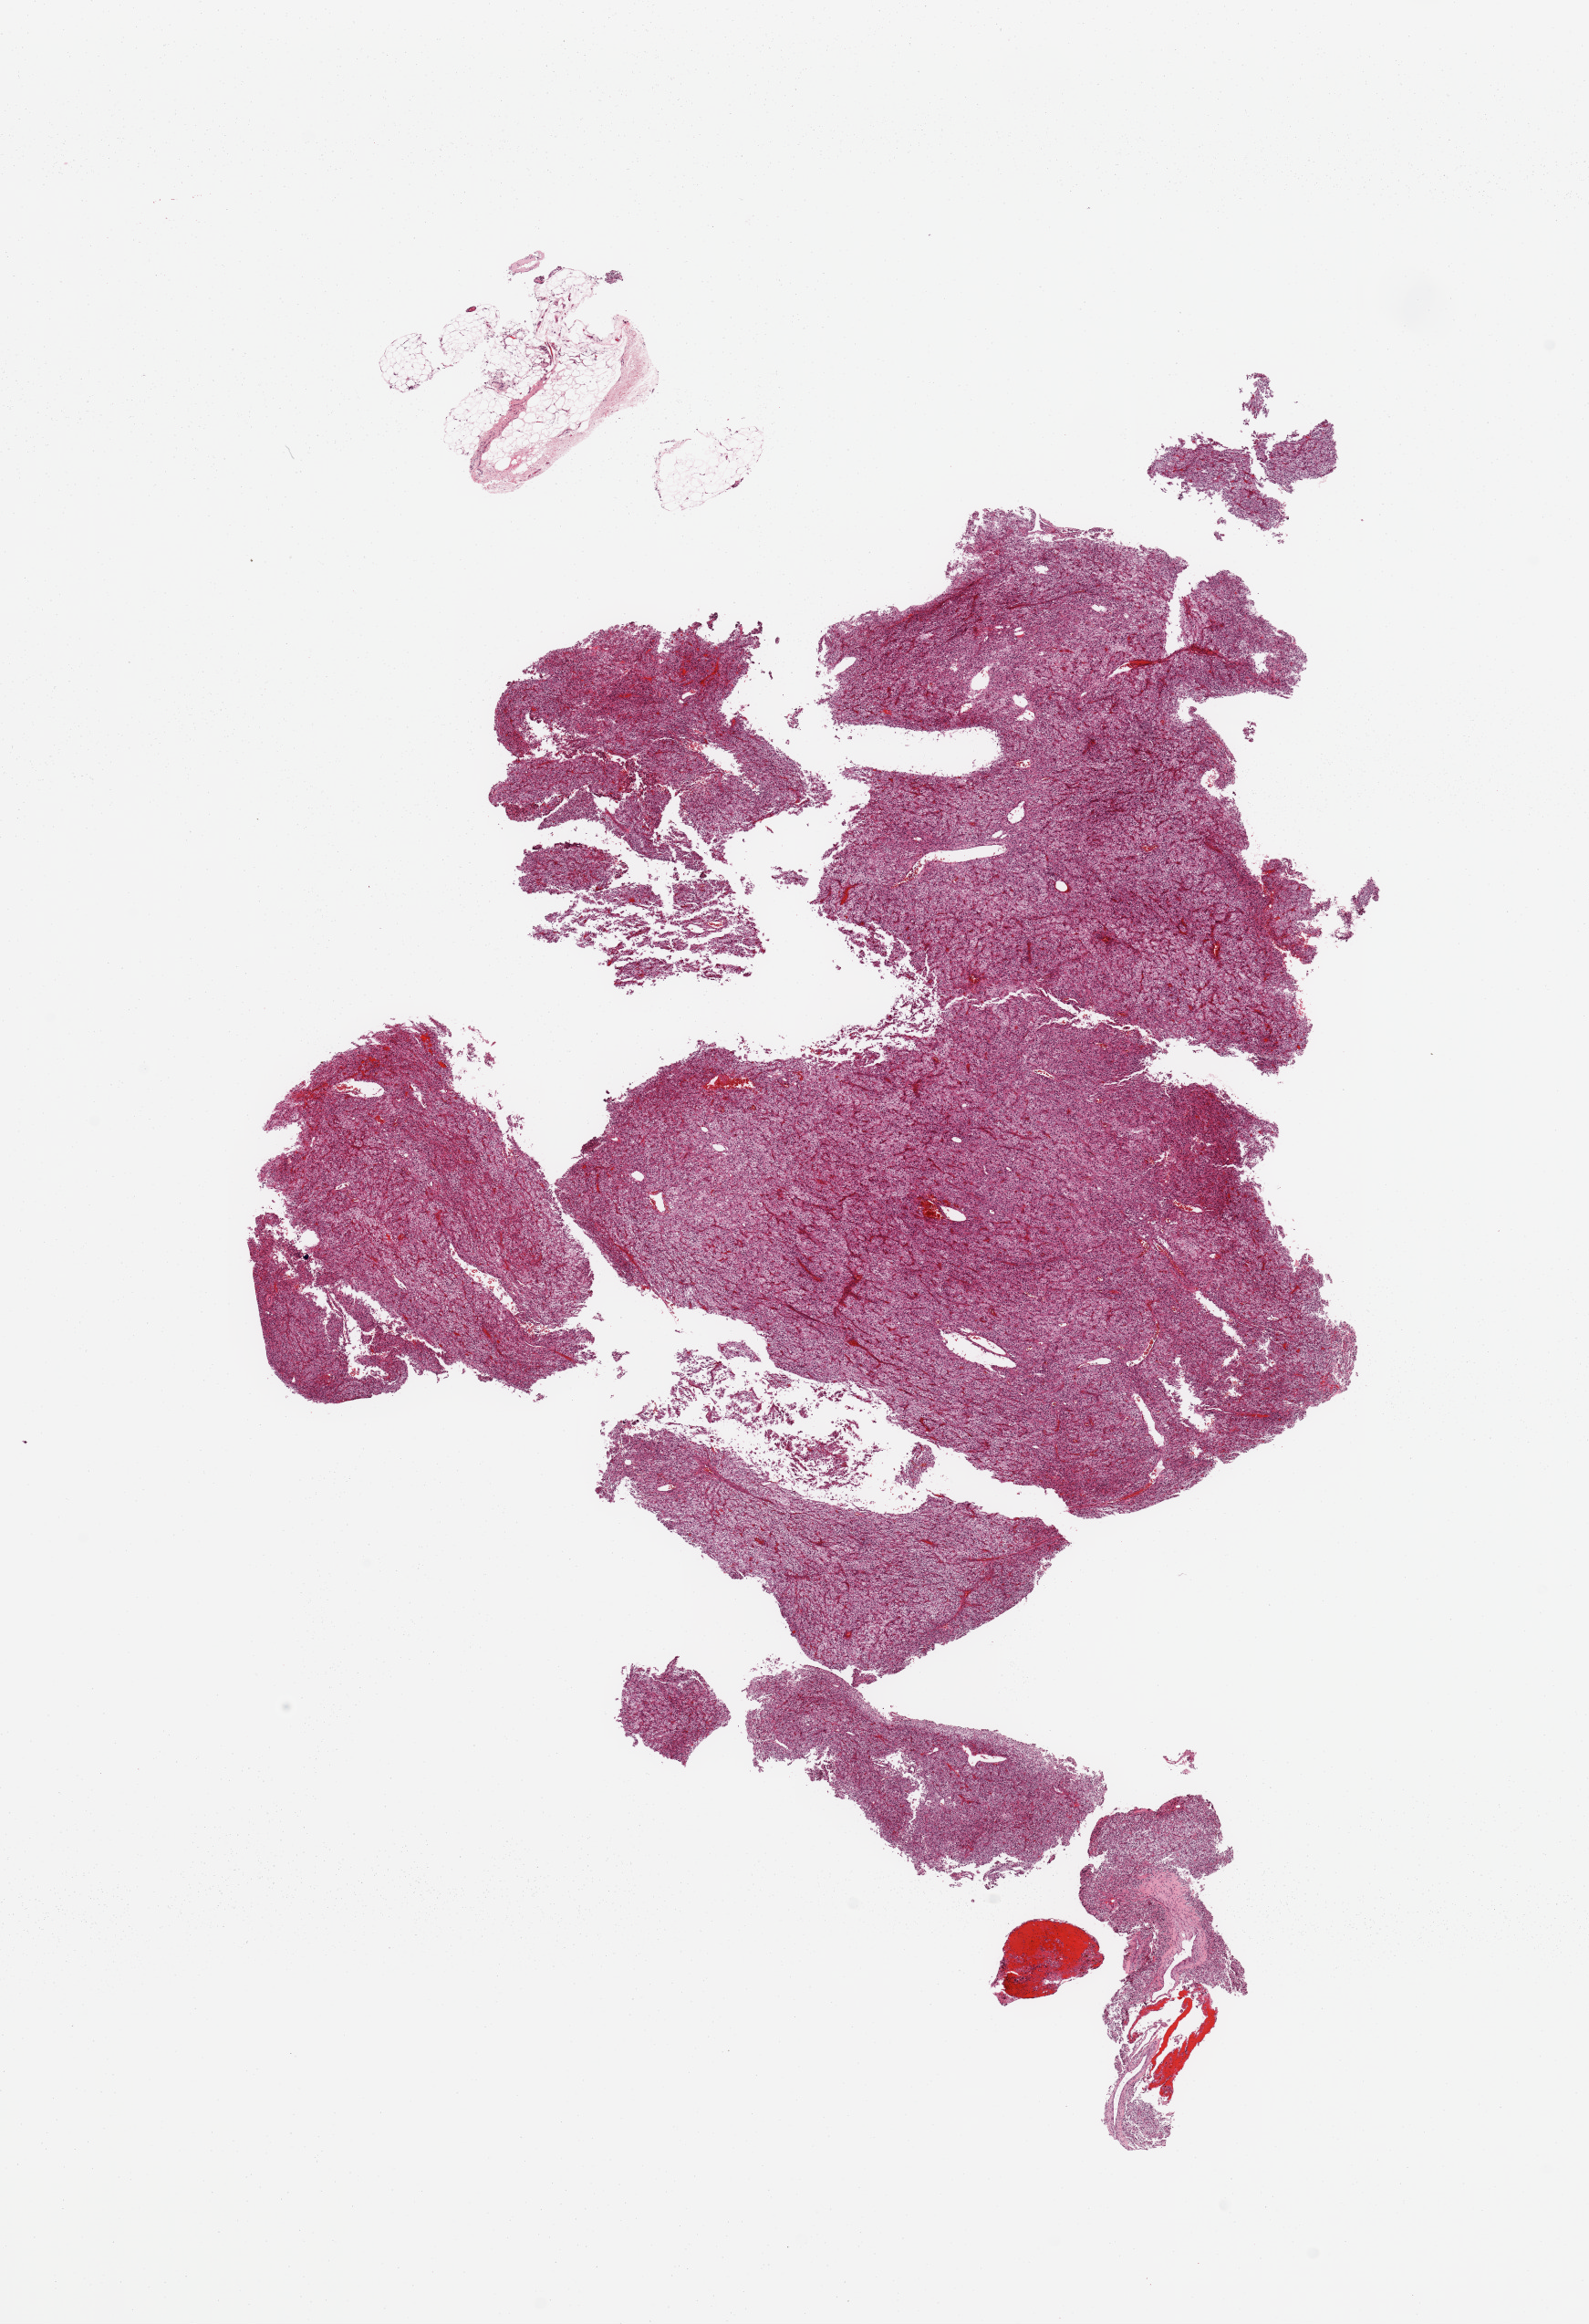
Whole-slide histology image, H&E — whole scanned area (about 13.8 x 20.2 mm, acquisition: 20x scan) shown as a low-resolution overview, tumour tissue sample, sampled site: kidney. Patient: male, age 58 years. Histologic grade: G3 (poorly differentiated). Pathologist review of this section (percent, as recorded): tumour nuclei 90%, necrosis 0%.
AJCC pathologic stage: III. Diagnosis: Renal cell carcinoma, NOS.